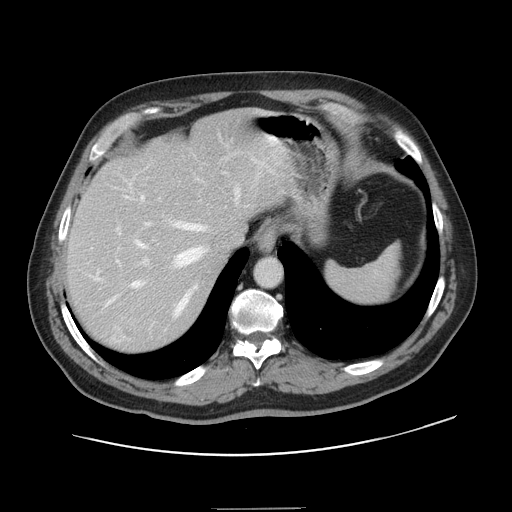
Contrast-enhanced abdominal CT, one axial slice; slice 113 of 143 in the series (ordered by position); soft-tissue window (W 400 / L 40 HU); 2.5 mm slice thickness; 512 × 512 image matrix, field of view 402 × 402 mm. Male patient, age 62 years. From the clinical record (not read from this slice): diagnosis: colorectal cancer liver metastases, imaged before liver resection; multiple liver metastases: yes; largest metastasis: 2.7 cm; disease in both lobes: no.
Structures marked on this image (manually delineated by an expert):
- hepatic veins: bounding box <95,188,240,315> (left, top, right, bottom; pixels)
- liver: <67,115,290,353>
- planned liver remnant (the part of the liver to remain after resection): <67,115,290,282>
- portal vein (with intrahepatic branches): <115,158,263,341>
- liver metastasis: <125,331,131,336>